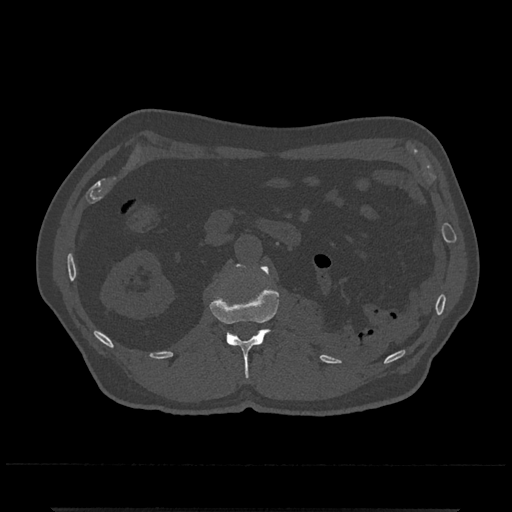
CT including the spine, one axial slice; position 347 of 797 along the scan axis; reconstruction kernel Br40s/3; 120 kVp; bone window (W 1800 / L 400 HU); 0.5 mm slice thickness; 512 × 512 image matrix, field of view 393 × 393 mm. Patient: male, 67 years. Case-level facts recorded for this patient, not image findings: primary cancer: prostate.
Structures marked on this image (semi-automatically segmented with operator editing):
- L1 vertebra: bounding box [x1, y1, x2, y2] px = [210, 264, 279, 378]
- L2 vertebra: [238, 264, 244, 268]